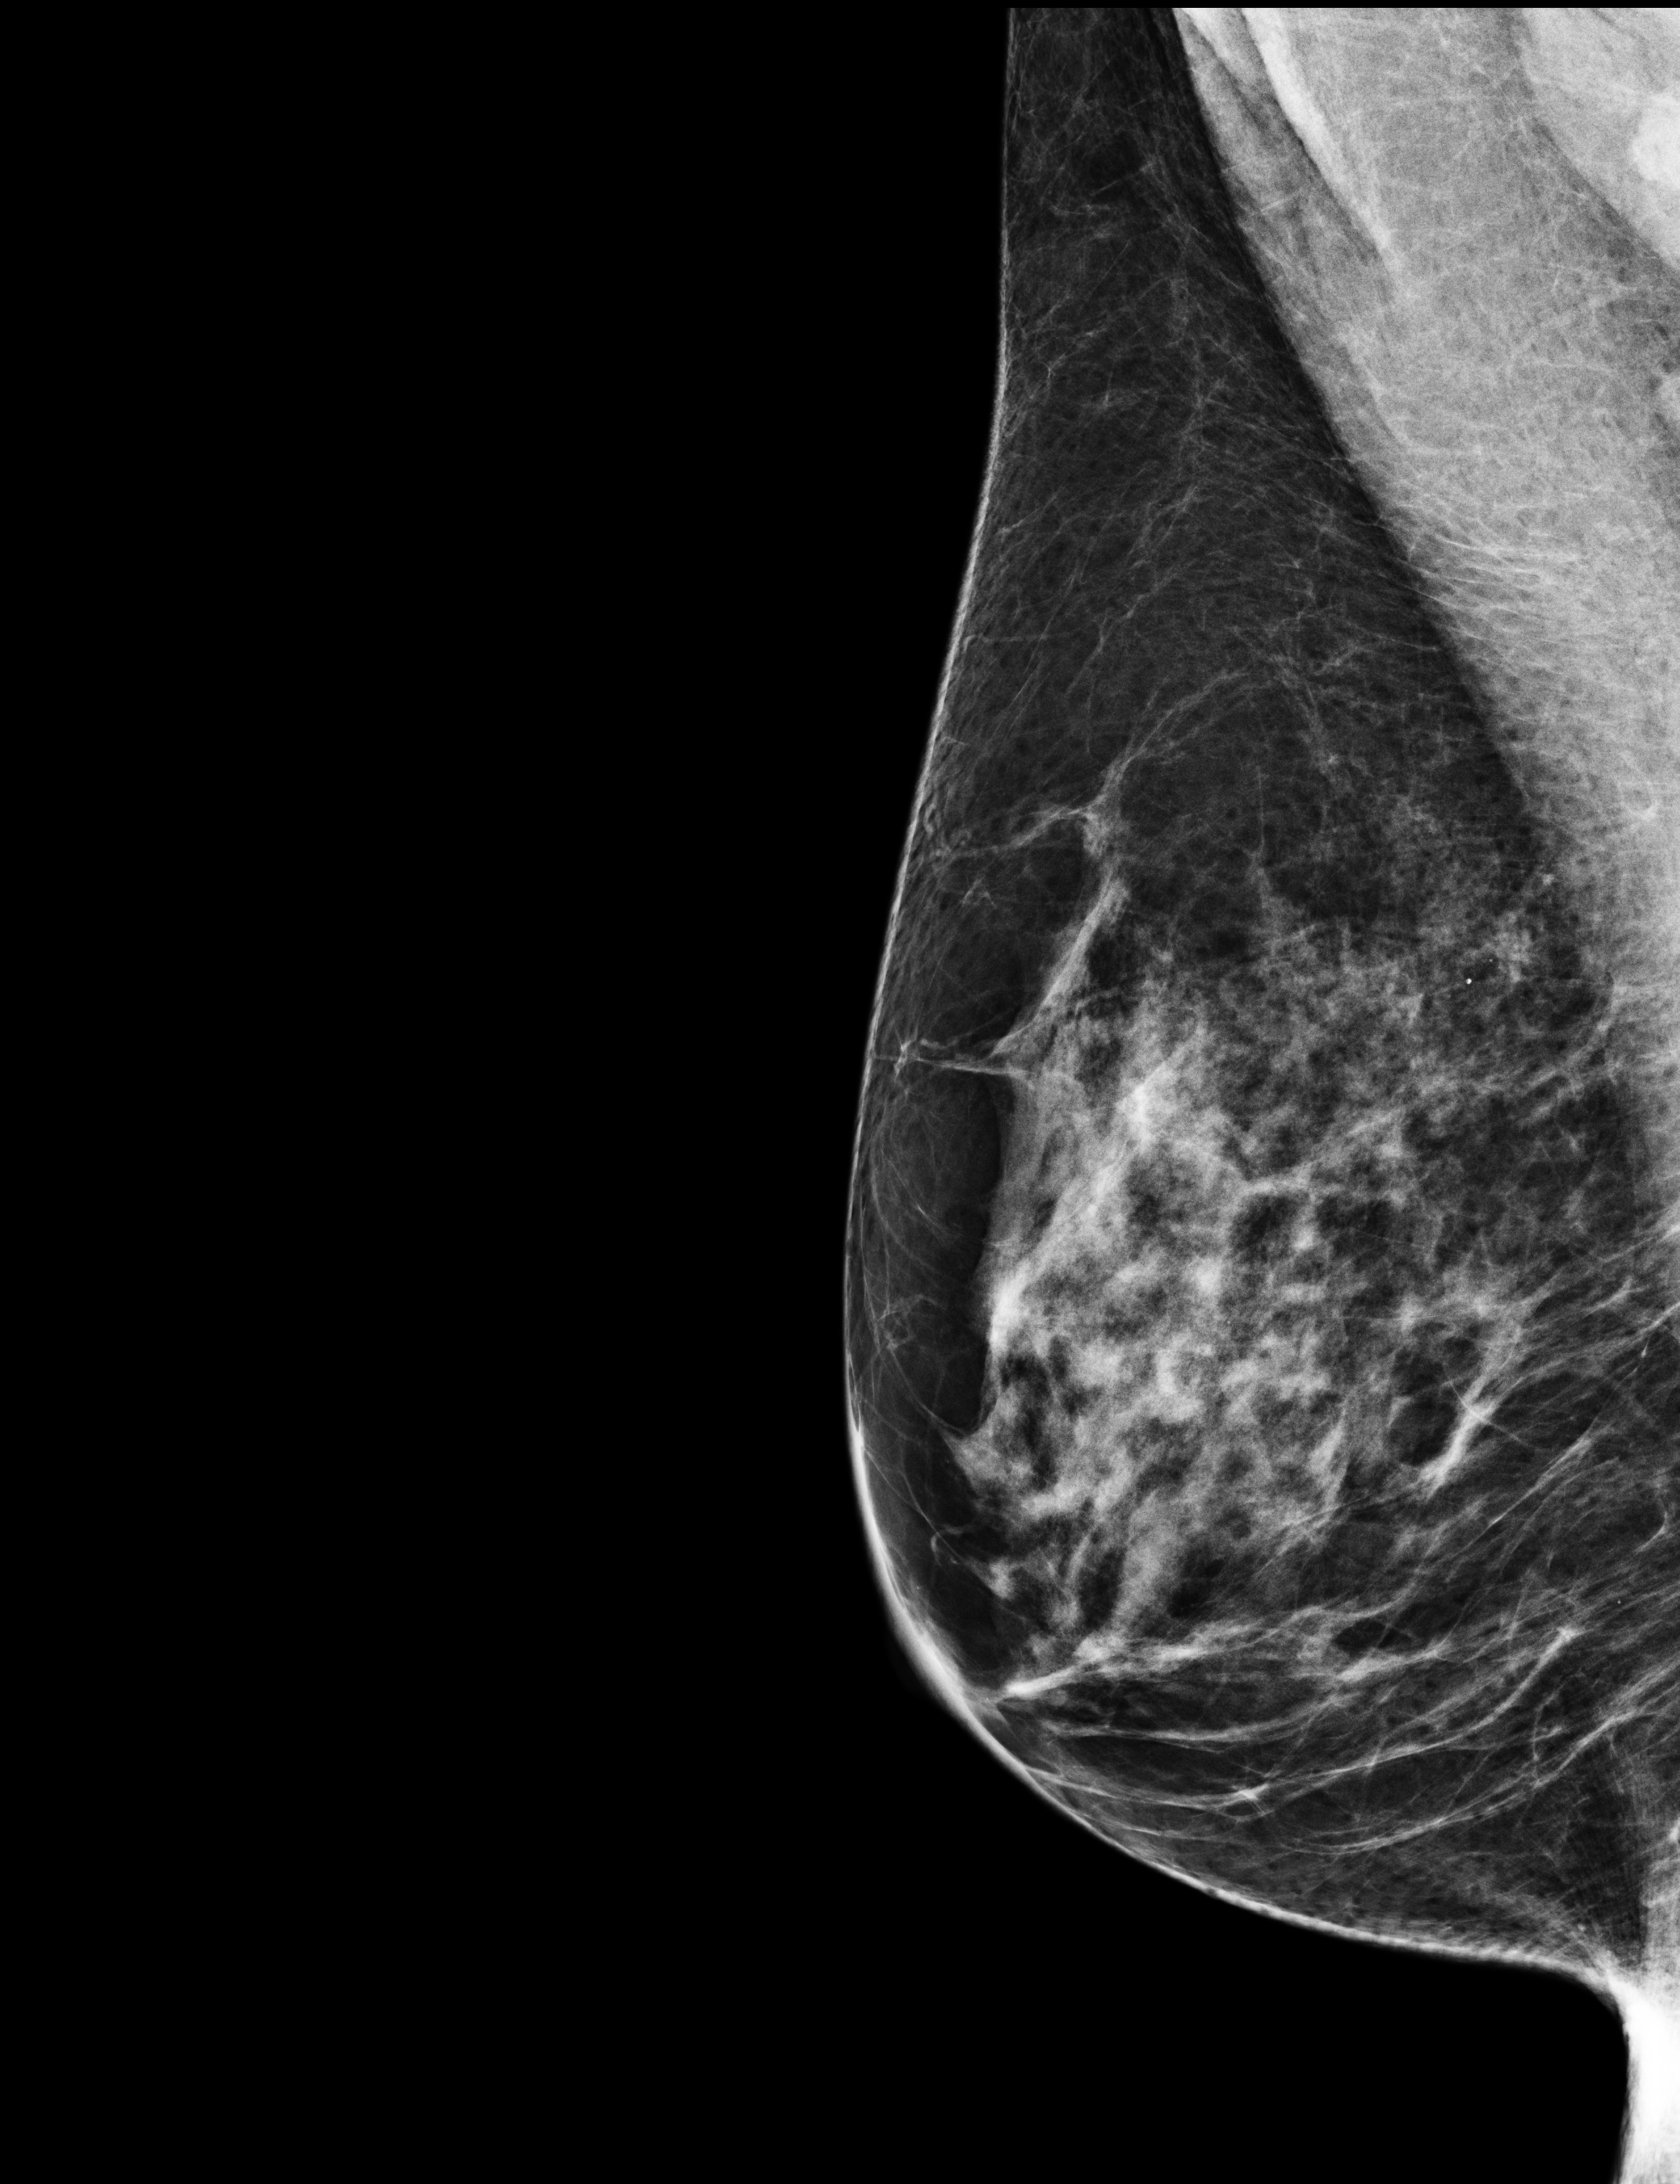
Digital mammogram (FFDM), right breast, mediolateral oblique (MLO) view, annual screening mammography examination, compressed breast thickness 54 mm, system: Selenia Dimensions. Patient: female, 66 years.
Breast density at the screening exam (both breasts): heterogeneously dense (BI-RADS density category c). Final BI-RADS category for the screening round (tomosynthesis exam, both breasts): category 1. Recall: no recall after this screen.